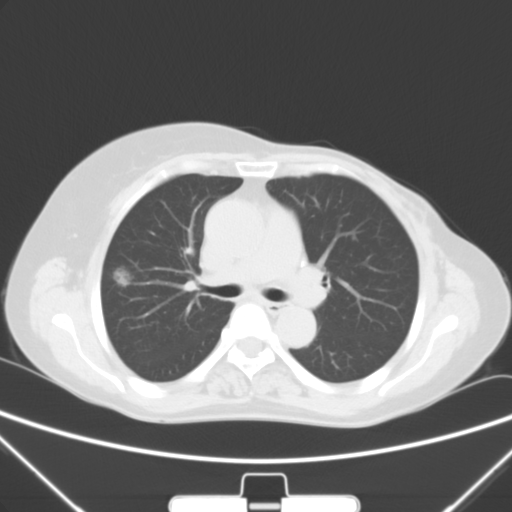
Chest CT, one axial slice; slice 32 of 53 in the series (ordered by position); lung window (W 1500 / L -600 HU); 5 mm slice thickness; 512 × 512 image matrix. Female patient, age 64 years. Case-level facts recorded for this patient, not image findings: clinical TNM (as recorded): T1c N0 M0.
Outlined on this slice (bounding box drawn by a radiologist):
- lung tumour (recorded histology: adenocarcinoma): box from (x=101, y=256) to (x=139, y=297) px